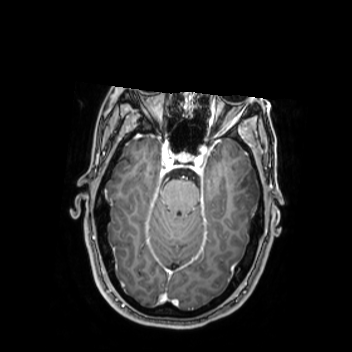
Brain MRI from a brain-tumour surgery series, one axial slice; slice 169 of 350 in the series (ordered by position); T1-weighted post-contrast; 0.9 mm slice thickness; 352 × 352 image matrix, field of view 280 × 280 mm. Case-level facts recorded for this patient, not image findings: histopathology: Oligodendroglioma; WHO grade: 2; IDH mutation: yes.
Structures marked on this image (manually delineated by an expert):
- tumour: bounding box <224,163,262,218> (left, top, right, bottom; pixels)